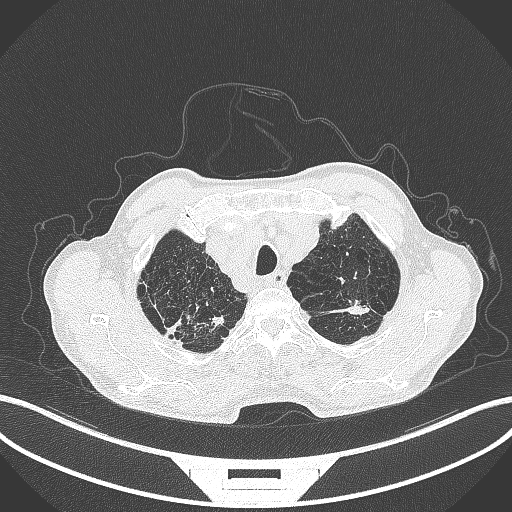
Chest CT, one axial slice; position 388 of 463 along the scan axis; reconstruction kernel B70f; 120 kVp; lung window (W 1500 / L -600 HU); 1 mm slice thickness; 512 × 512 image matrix, field of view 400 × 400 mm. Patient: male, 74 years. Case-level facts recorded for this patient, not image findings: clinical TNM (as recorded): T2a N1 M0.
Outlined on this slice (rectangle marked by the reading radiologist):
- lung tumour (recorded histology: adenocarcinoma): bounding box (x1, y1, x2, y2) in pixels: (330, 300, 373, 318)